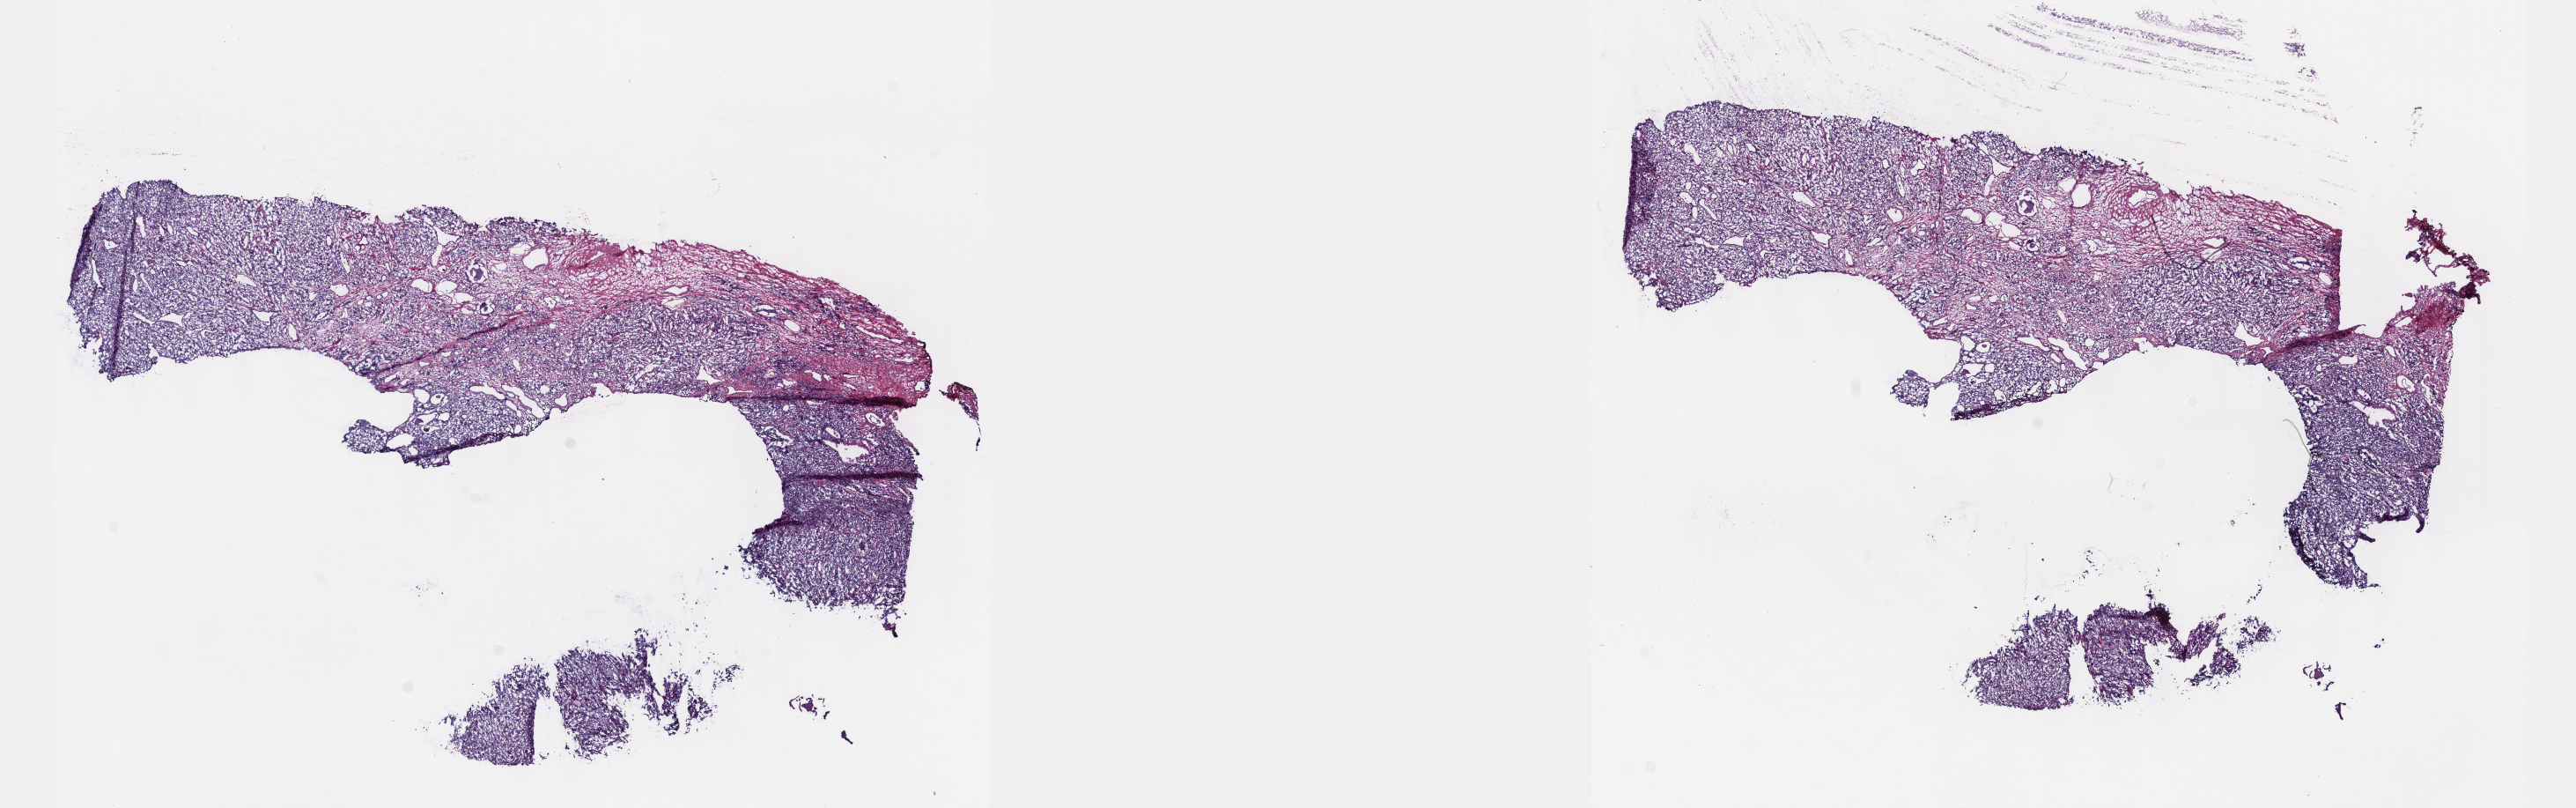
Whole-slide histology image, H&E-stained, shown as a low-resolution overview of the whole scanned area (about 23.6 x 7.4 mm, slide scanned at 40x); frozen section from the top of the tissue portion; sample: primary tumour, prostate. Male, age 68 years at initial diagnosis. Gleason score: 9 (4+5). Pathologist review of this section (percent, as recorded): tumour cells 62%, tumour nuclei 90%, normal cells 3%, stromal cells 33%, necrosis 2%. Inflammatory infiltration, as recorded: lymphocyte infiltration 3%, monocyte infiltration 0%, neutrophil infiltration 0%.
• pathologic diagnosis: Adenocarcinoma, NOS (prostate gland)